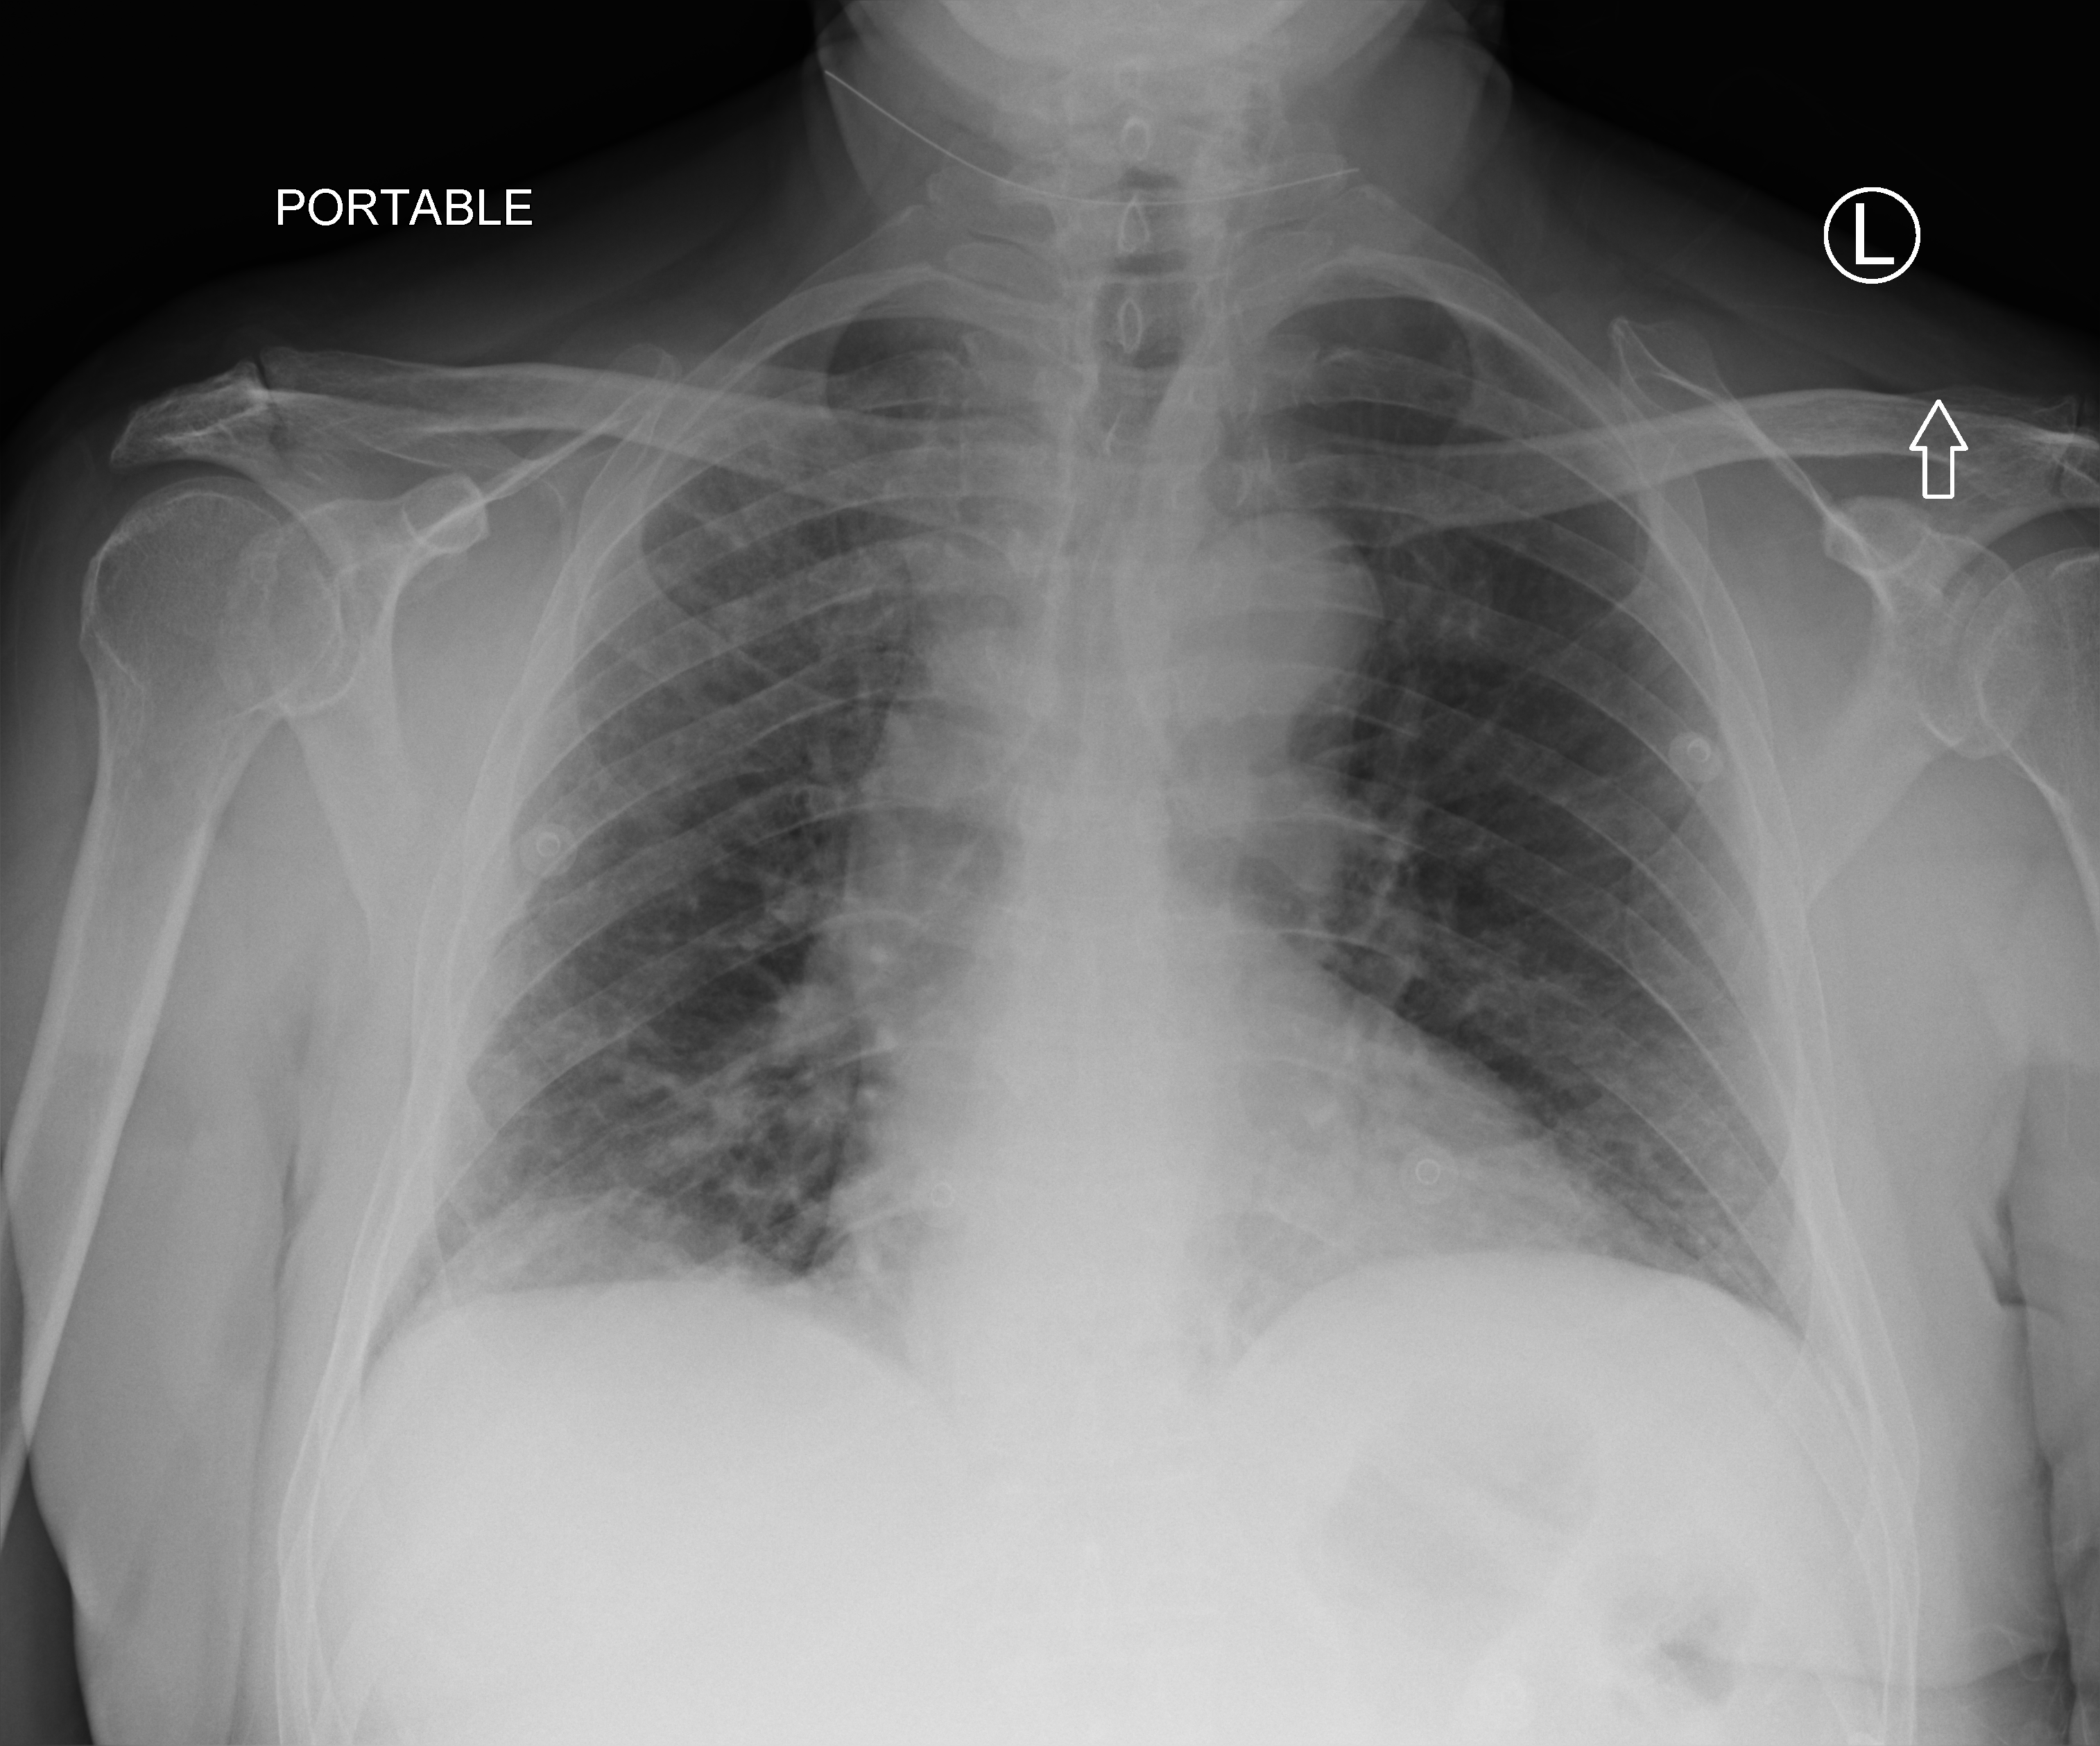
Bedside chest radiograph (computed radiography). Patient hospitalised with COVID-19; male, aged 60–74 years.
Hospital-stay facts (about this admission, not read from this image; timing relative to this image not recorded): length of hospital stay: 3 days.